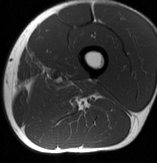
MRI of an extremity soft-tissue mass, one axial slice; position 19 of 70 along the scan axis; MR volume resampled by the dataset authors to the PET/CT grid (not the native acquisition matrix); 157 × 163 image matrix, field of view 153 × 159 mm. Male patient. From the clinical record (not read from this slice): histological type: extraskeletal osteosarcoma; grade: high; site of the primary tumour: left adductur.
Annotated regions visible in this slice (expert contour drawn on MRI and transferred to this co-registered scan by the dataset authors):
- gross tumour volume (mass): bounding box <31,78,95,102> (left, top, right, bottom; pixels)